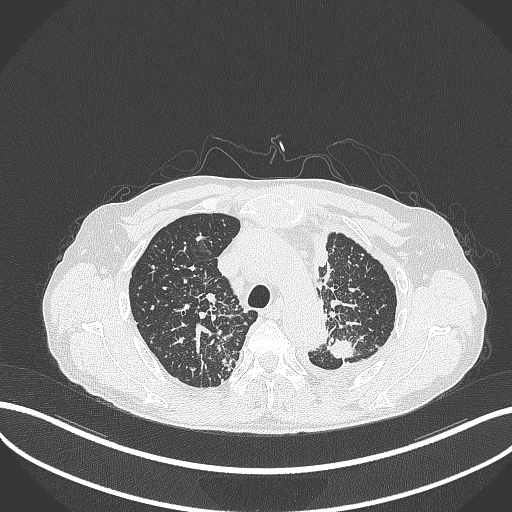
Chest CT, one axial slice. Position 266 of 325 along the scan axis. Reconstruction kernel B70f. 120 kVp. Lung window (W 1500 / L -600 HU). 1 mm slice thickness. 512 × 512 image matrix, field of view 400 × 400 mm. Patient: male, 58 years. From the clinical record (not read from this slice): clinical TNM (as recorded): T1c N3 M1.
Structures marked on this image (rectangle marked by the reading radiologist):
- lung tumour (recorded histology: adenocarcinoma): bounding box [x1, y1, x2, y2] px = [324, 335, 359, 363]